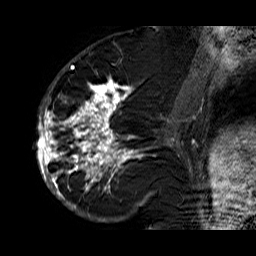
Breast MRI (dynamic contrast-enhanced), one sagittal slice. Dynamic contrast-enhanced series, time point 2 of 6 at this slice position (early post-contrast). 1.5 T. TE 6.3 ms, TR 32.9 ms. 4 mm slice thickness. 256 × 256 image matrix, field of view 200 × 200 mm. Female patient. From the clinical record (not read from this slice): setting: breast cancer imaged before/during neoadjuvant chemotherapy; receptor status: HR-positive, HER2-negative.
Structures marked on this image (semi-automatic segmentation, software-assisted and operator-edited):
- analysis volume of interest (the breast-tissue region the enhancement analysis was run in; not a lesion): bounding box <36,74,176,210> (left, top, right, bottom; pixels)
- tumour enhancement mask (voxels above the 100 % enhancement threshold inside the analysis volume of interest): <36,79,176,210>